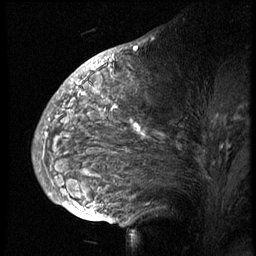
Breast MRI (dynamic contrast-enhanced), one sagittal slice. Position 36 of 74 along the scan axis. 3 images stored at this slice position (order not interpretable as contrast timing). 1.5 T. TE 4.2 ms, TR 8.9 ms. 2.5 mm slice thickness. 256 × 256 image matrix, field of view 200 × 200 mm. Patient: female, 57 years. From the clinical record (not read from this slice): setting: breast cancer imaged before/during neoadjuvant chemotherapy; receptor status: HER2-positive.
Outlined on this slice (semi-automatically segmented with operator editing):
- analysis volume of interest (the breast-tissue region the enhancement analysis was run in; not a lesion): bounding box [x1, y1, x2, y2] px = [51, 67, 247, 173]
- tumour enhancement mask (voxels above the 140 % enhancement threshold inside the analysis volume of interest): [93, 67, 143, 134]